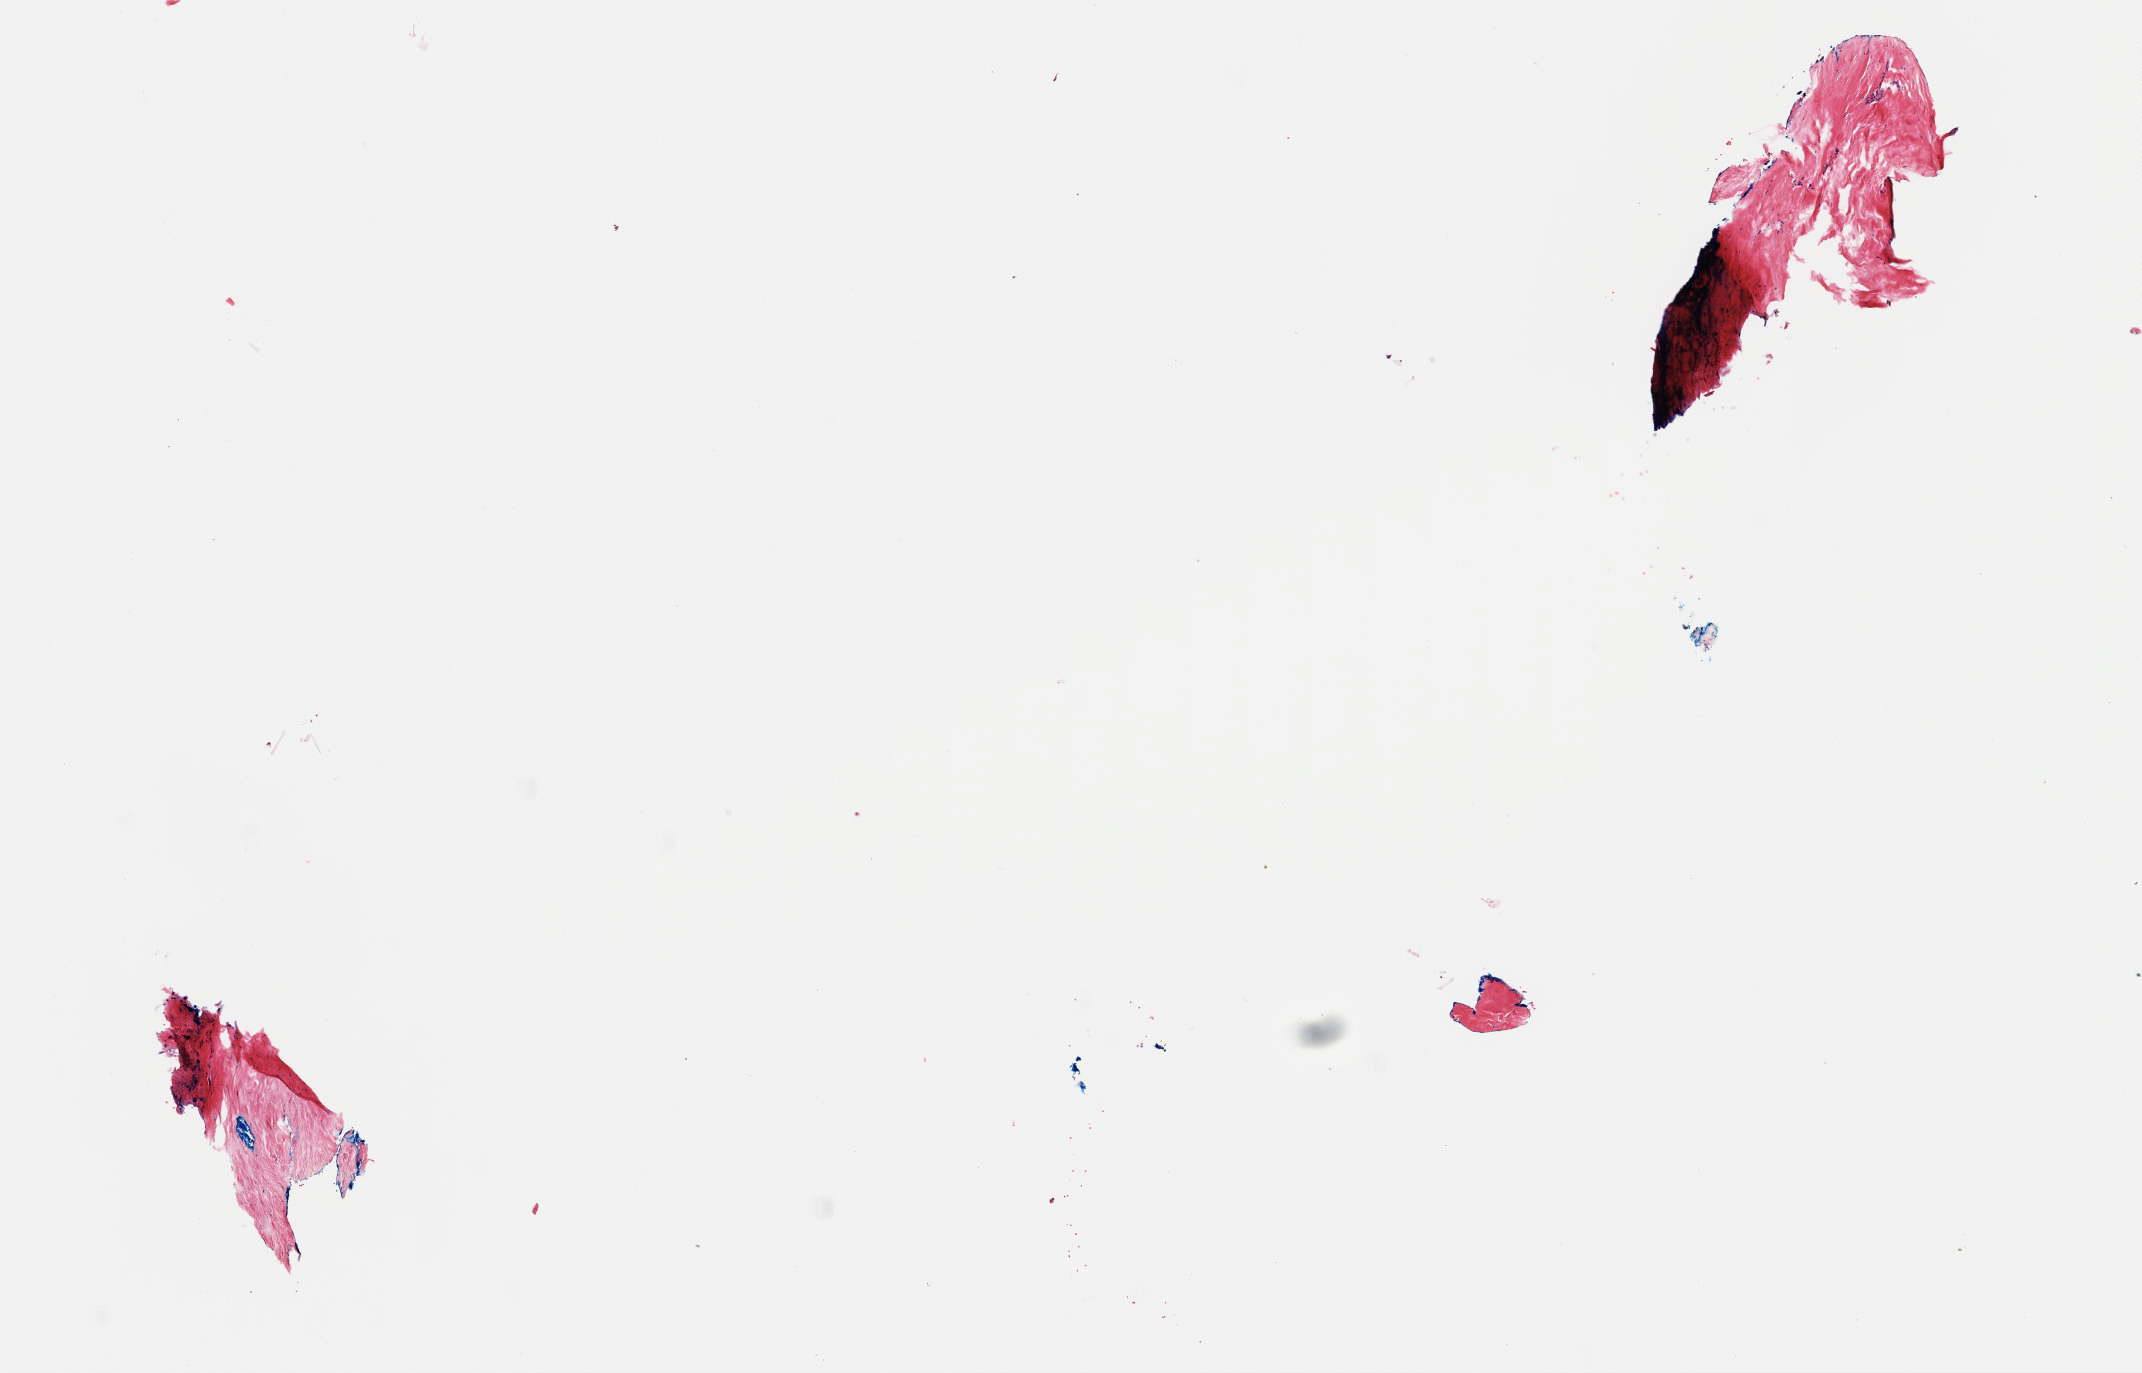
Whole-slide histology image, Hematoxylin and eosin (H&E) stained — shown as a low-resolution overview of the whole scanned area (about 8.5 x 5.4 mm, from a 40x scan), frozen section, sample: primary tumour, breast. Female patient; age at initial diagnosis 53 years. Slide review estimates, as recorded: tumour cells 0%, tumour nuclei 0%, normal cells 0%, stromal cells 100%, necrosis 0%. Inflammatory infiltration, as recorded: lymphocyte infiltration 0%, monocyte infiltration 0%, neutrophil infiltration 0%.
Lymph nodes positive (case pathology): 0 of 5 examined. Histologic diagnosis: Lobular carcinoma, NOS. AJCC pathologic stage: IA.